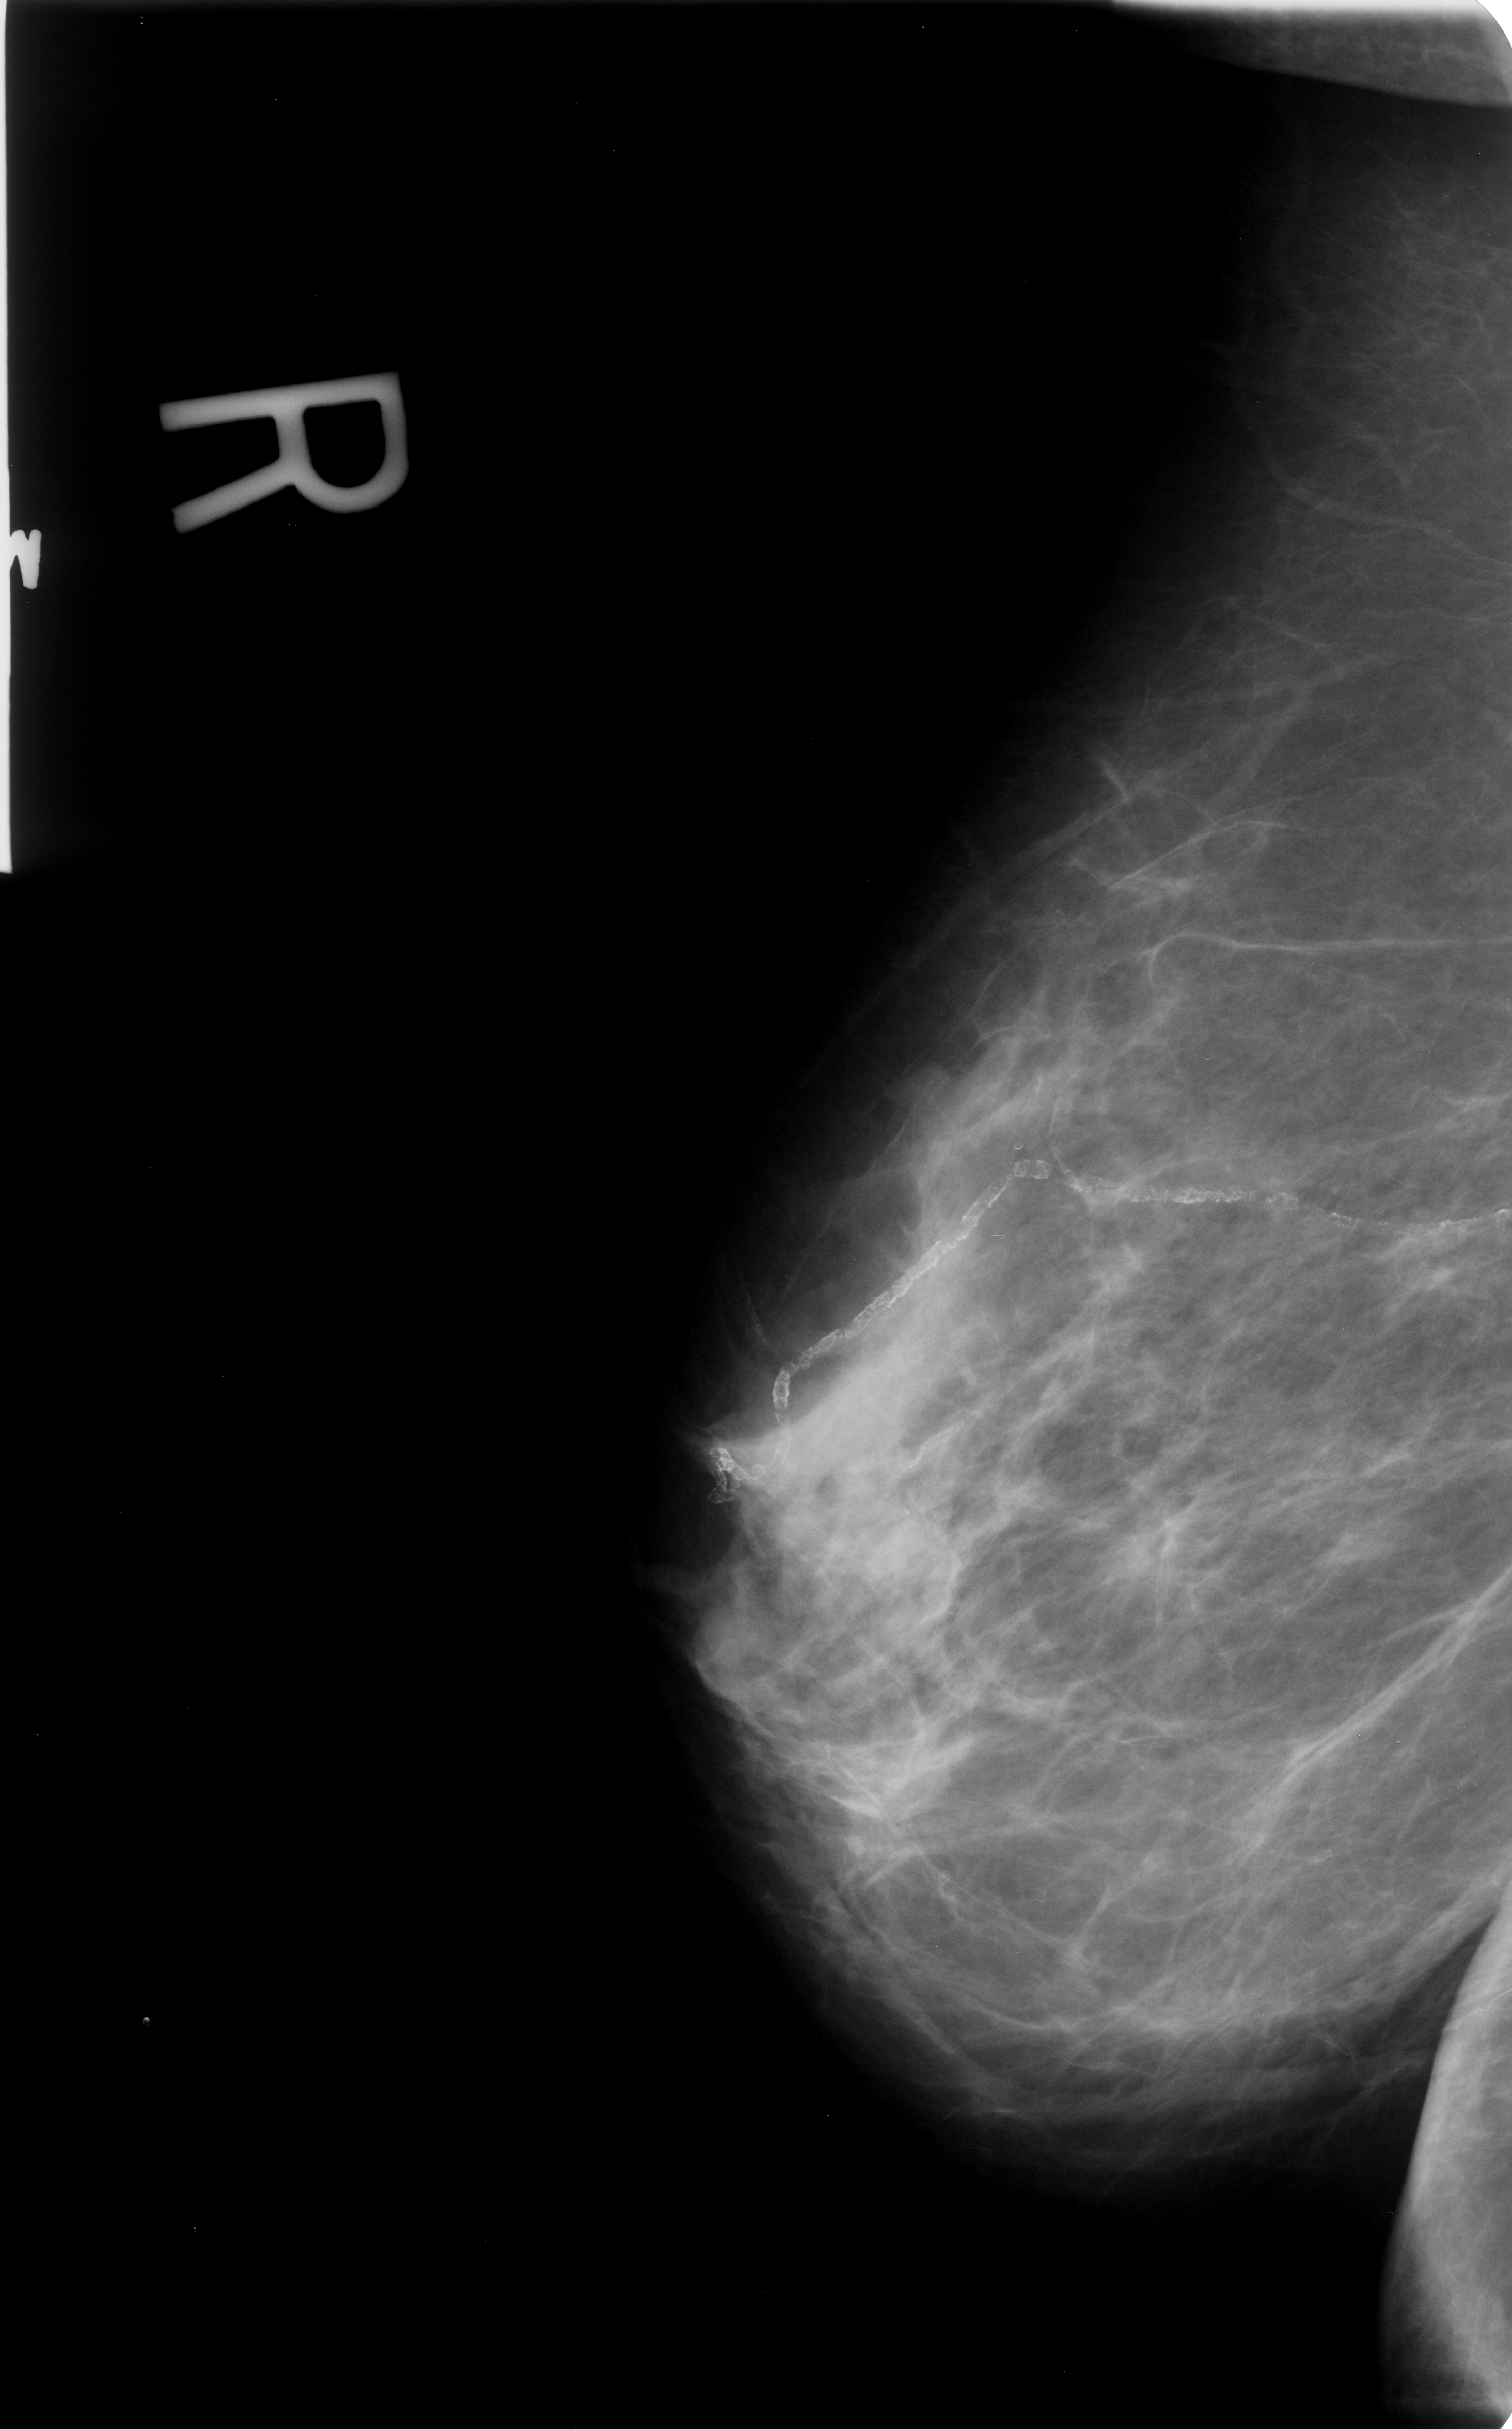
Digitized screen-film mammogram; right breast; mediolateral oblique (MLO) view; breast composition: scattered fibroglandular densities (BI-RADS density category 2 of 4).
Finding: calcifications, morphology vascular; BI-RADS assessment category 2; subtlety rating 5 on a 1 (subtle) to 5 (obvious) scale; benign without callback (not worked up further).